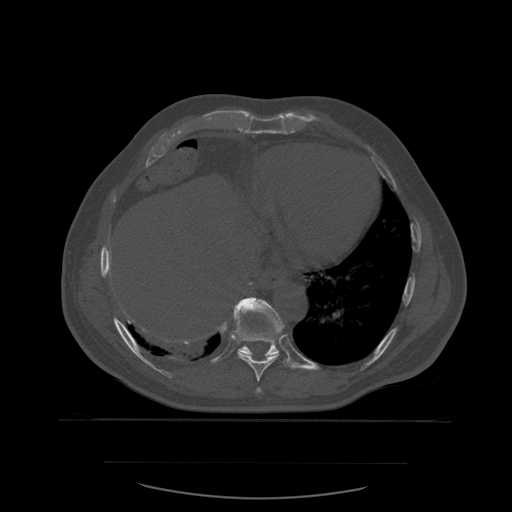
CT including the spine, one axial slice. Position 333 of 590 along the scan axis. Bone window (W 1800 / L 400 HU). 1.25 mm slice thickness. 512 × 512 image matrix, field of view 479 × 479 mm. Patient age 71 years. From the clinical record (not read from this slice): primary cancer: lung; vertebrae with lytic lesions (as recorded): T1, T2, L5, S1.
Outlined on this slice (semi-automatic segmentation, software-assisted and operator-edited):
- T10 vertebra: bounding box <234,298,286,364> (left, top, right, bottom; pixels)
- T8 vertebra: <257,388,262,393>
- T9 vertebra: <234,302,279,382>